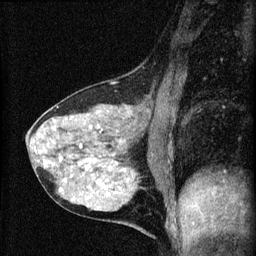
Breast MRI (dynamic contrast-enhanced), one sagittal slice. Position 25 of 60 along the scan axis. Dynamic contrast-enhanced series, image 2 of 4 at this slice position (ordered by acquisition). 1.5 T. TE 4.2 ms, TR 8.2 ms. 2 mm slice thickness. 256 × 256 image matrix. Patient: female, 41 years.
Outlined on this slice (semi-automatically segmented with operator editing):
- analysis volume of interest (the breast-tissue region the enhancement analysis was run in; not a lesion): bounding box [x1, y1, x2, y2] px = [26, 91, 166, 210]
- tumour enhancement mask (voxels above the 70 % enhancement threshold inside the analysis volume of interest): [34, 130, 101, 169]